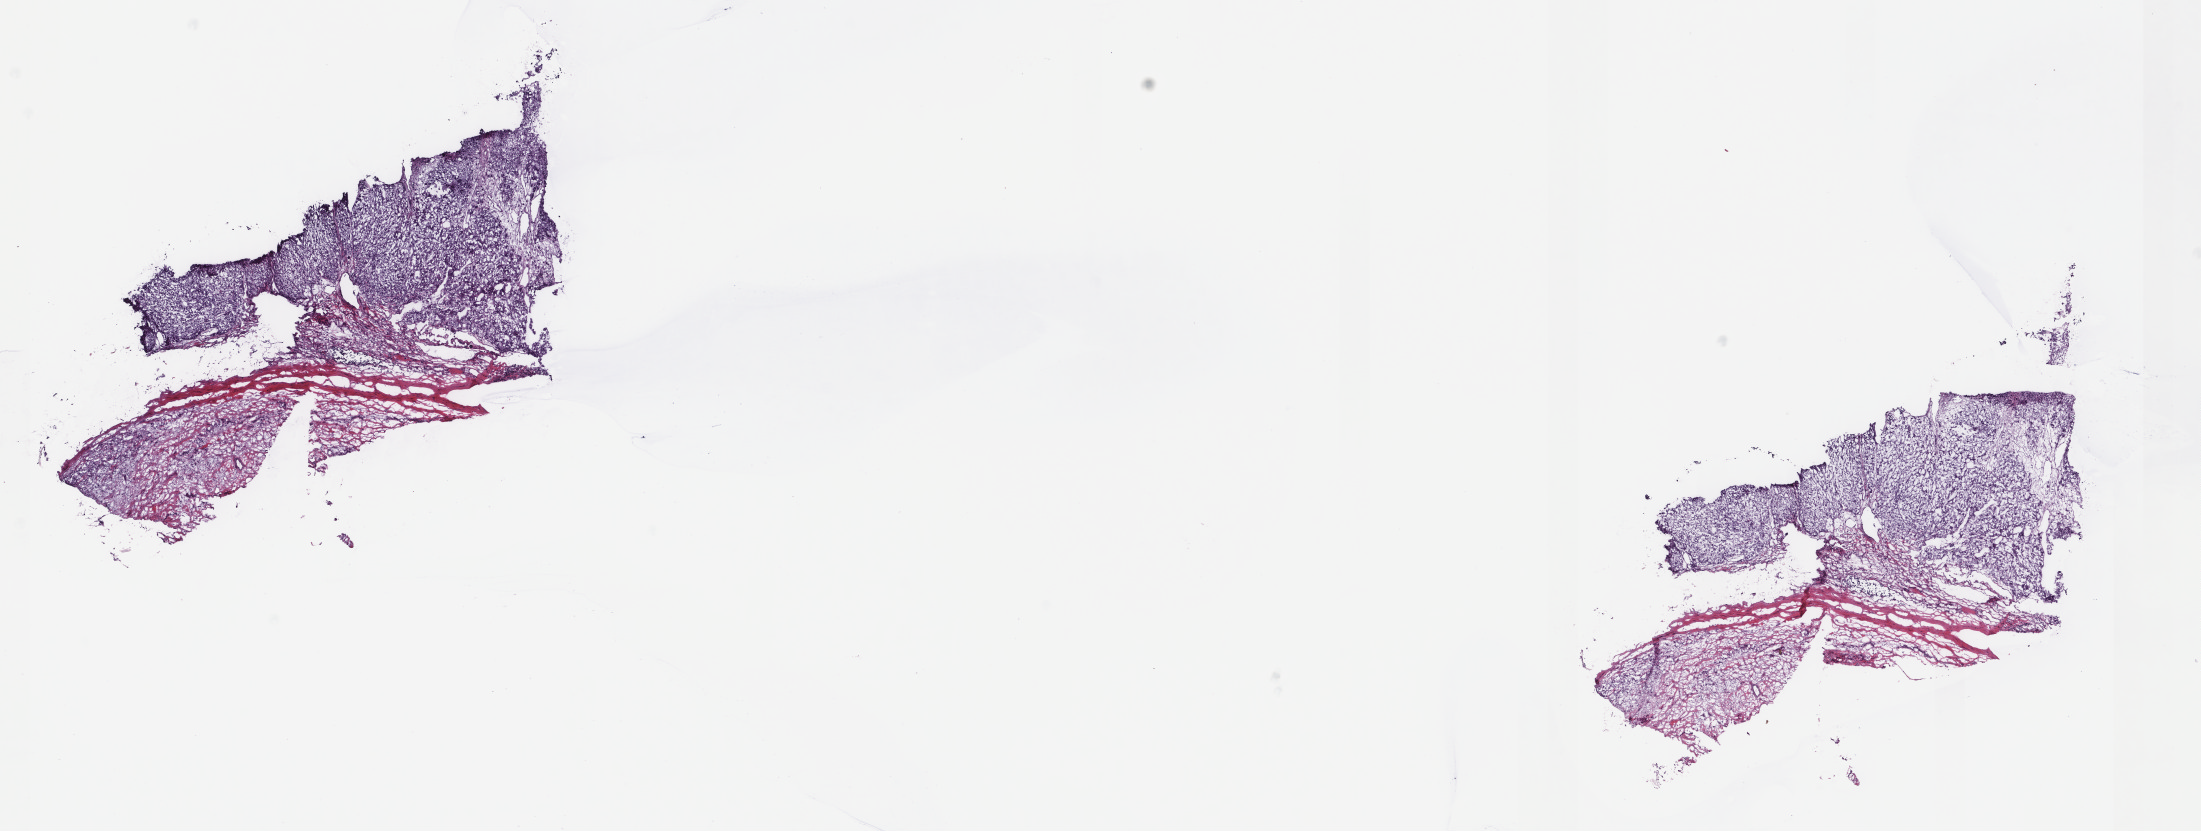
Hematoxylin and eosin (H&E) stained whole-slide image, shown as a low-resolution overview of the whole scanned area (about 17.5 x 6.6 mm). Frozen section. Metastatic tumour sample, sampled site: lymph node. Female, age 53 years at initial diagnosis. Pathologist review of this section (percent, as recorded): tumour cells 85%, tumour nuclei 85%.
This section: metastatic tumour tissue. Patient diagnosis: Malignant melanoma, NOS.